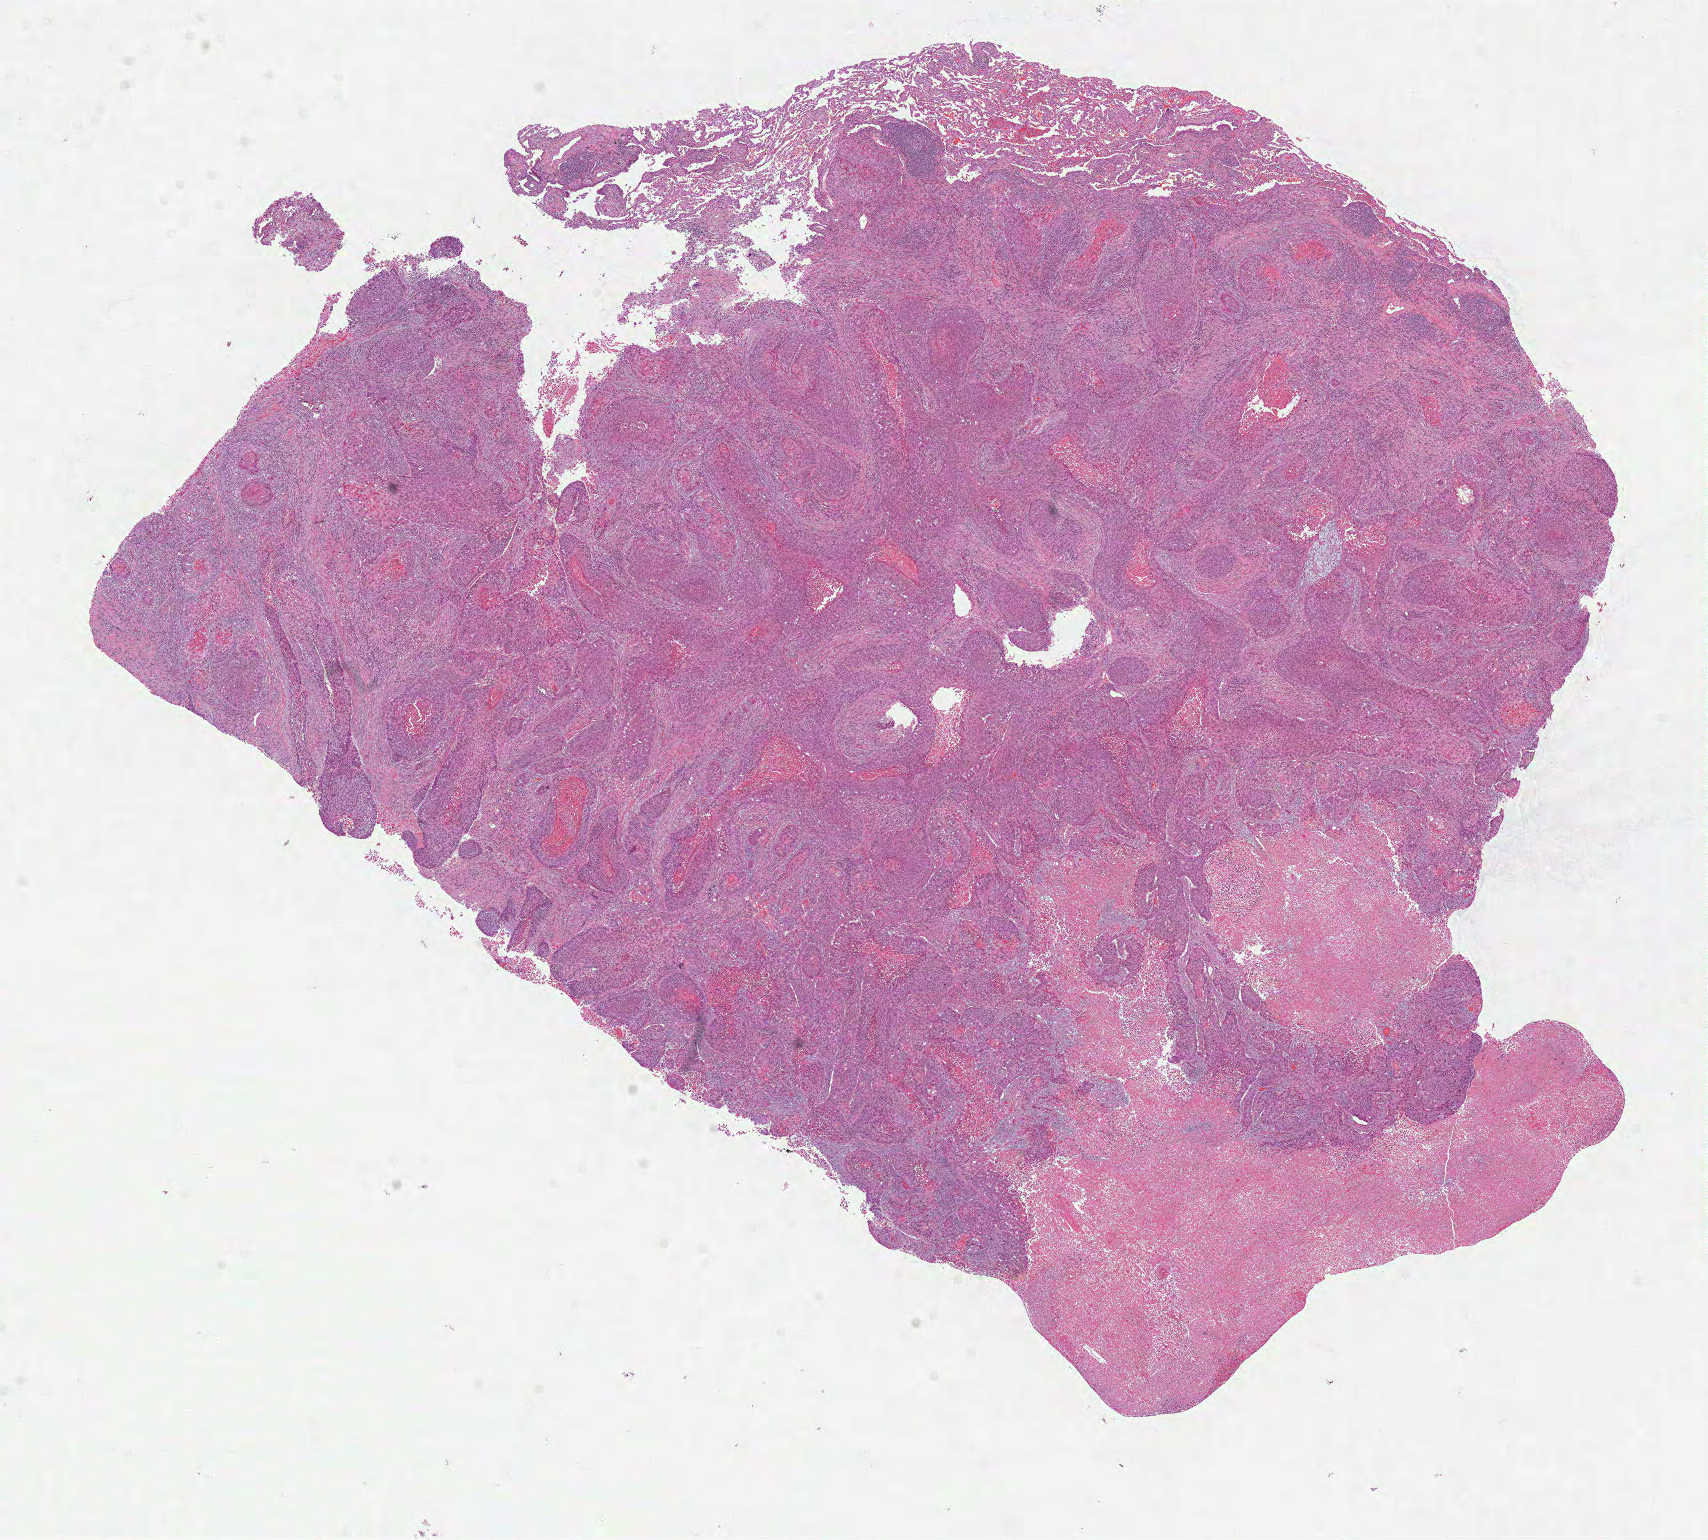
Digitized Hematoxylin and eosin (H&E) stained tissue section (whole slide), shown as a low-resolution overview of the whole scanned area (about 13.8 x 12.4 mm), formalin-fixed paraffin-embedded (FFPE) diagnostic section, sample: primary tumour, lung. Patient: male, age at initial diagnosis 83 years.
AJCC pathologic stage: IB (7th edition). Histologic diagnosis: Squamous cell carcinoma, NOS.